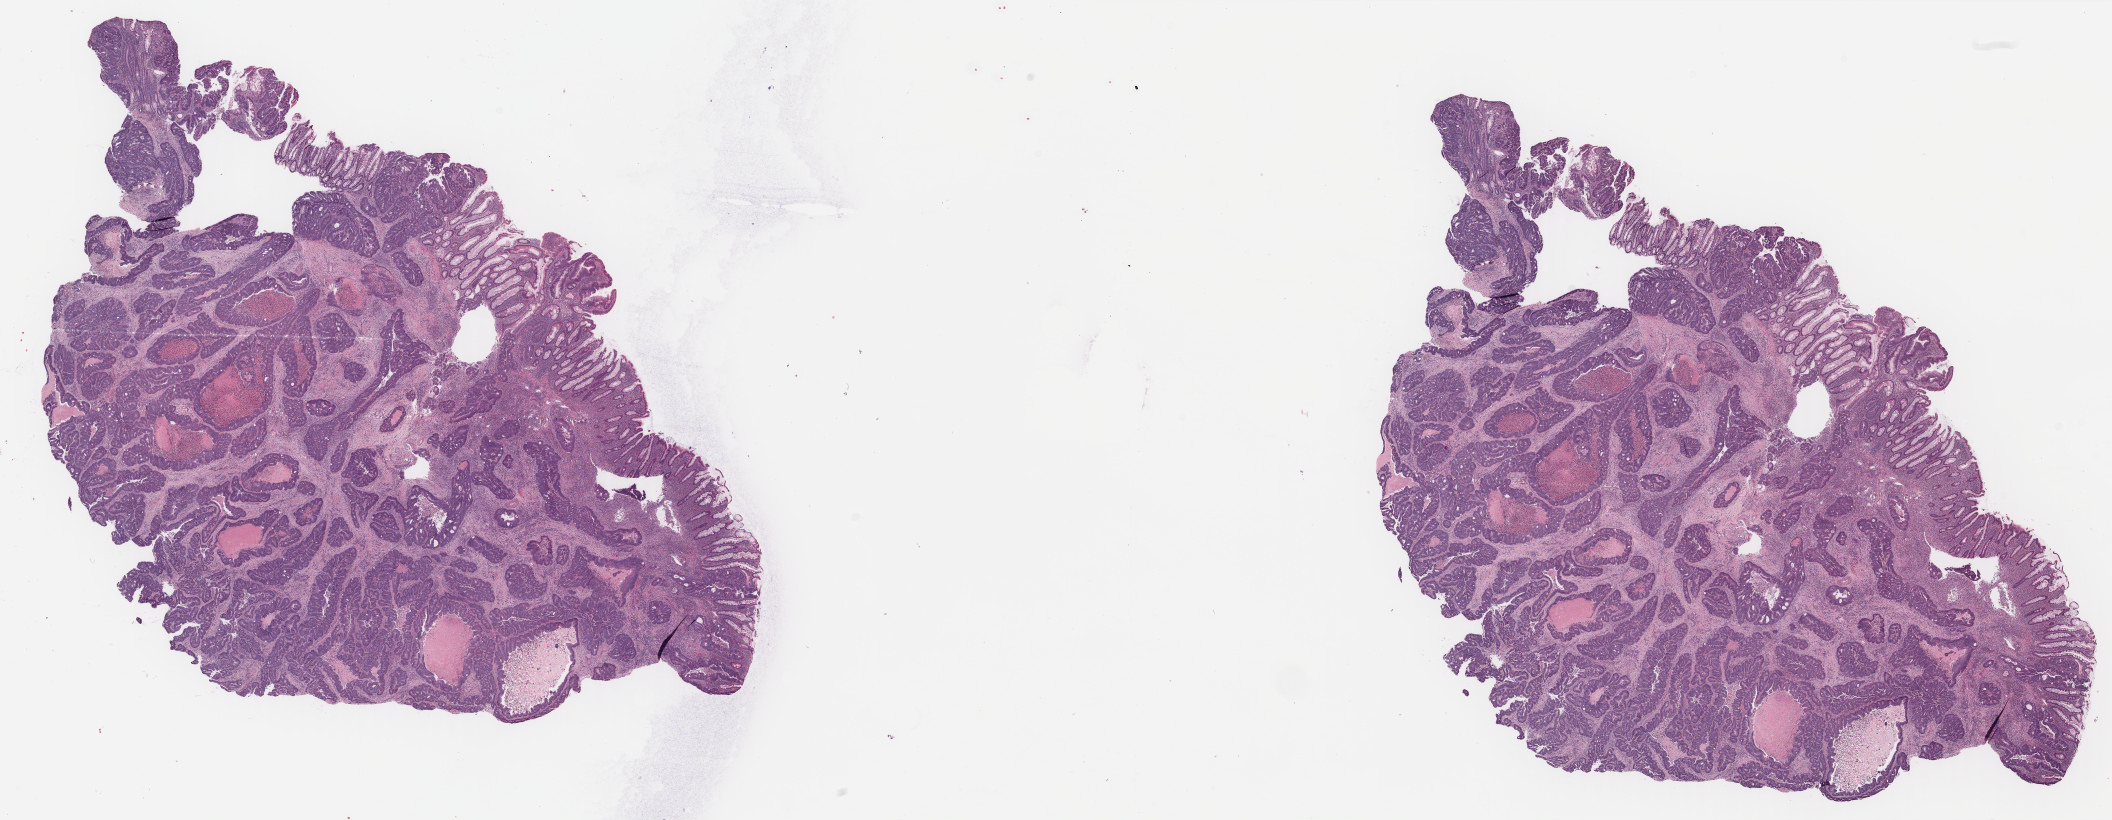
H&E whole-slide image, low-resolution overview of the scanned area, about 33.4 x 13.0 mm (from a 40x scan). FFPE section. Colon, primary tumour sample. Female, age 74 years at initial diagnosis.
Pathologic diagnosis: Adenocarcinoma, NOS (hepatic flexure of colon).